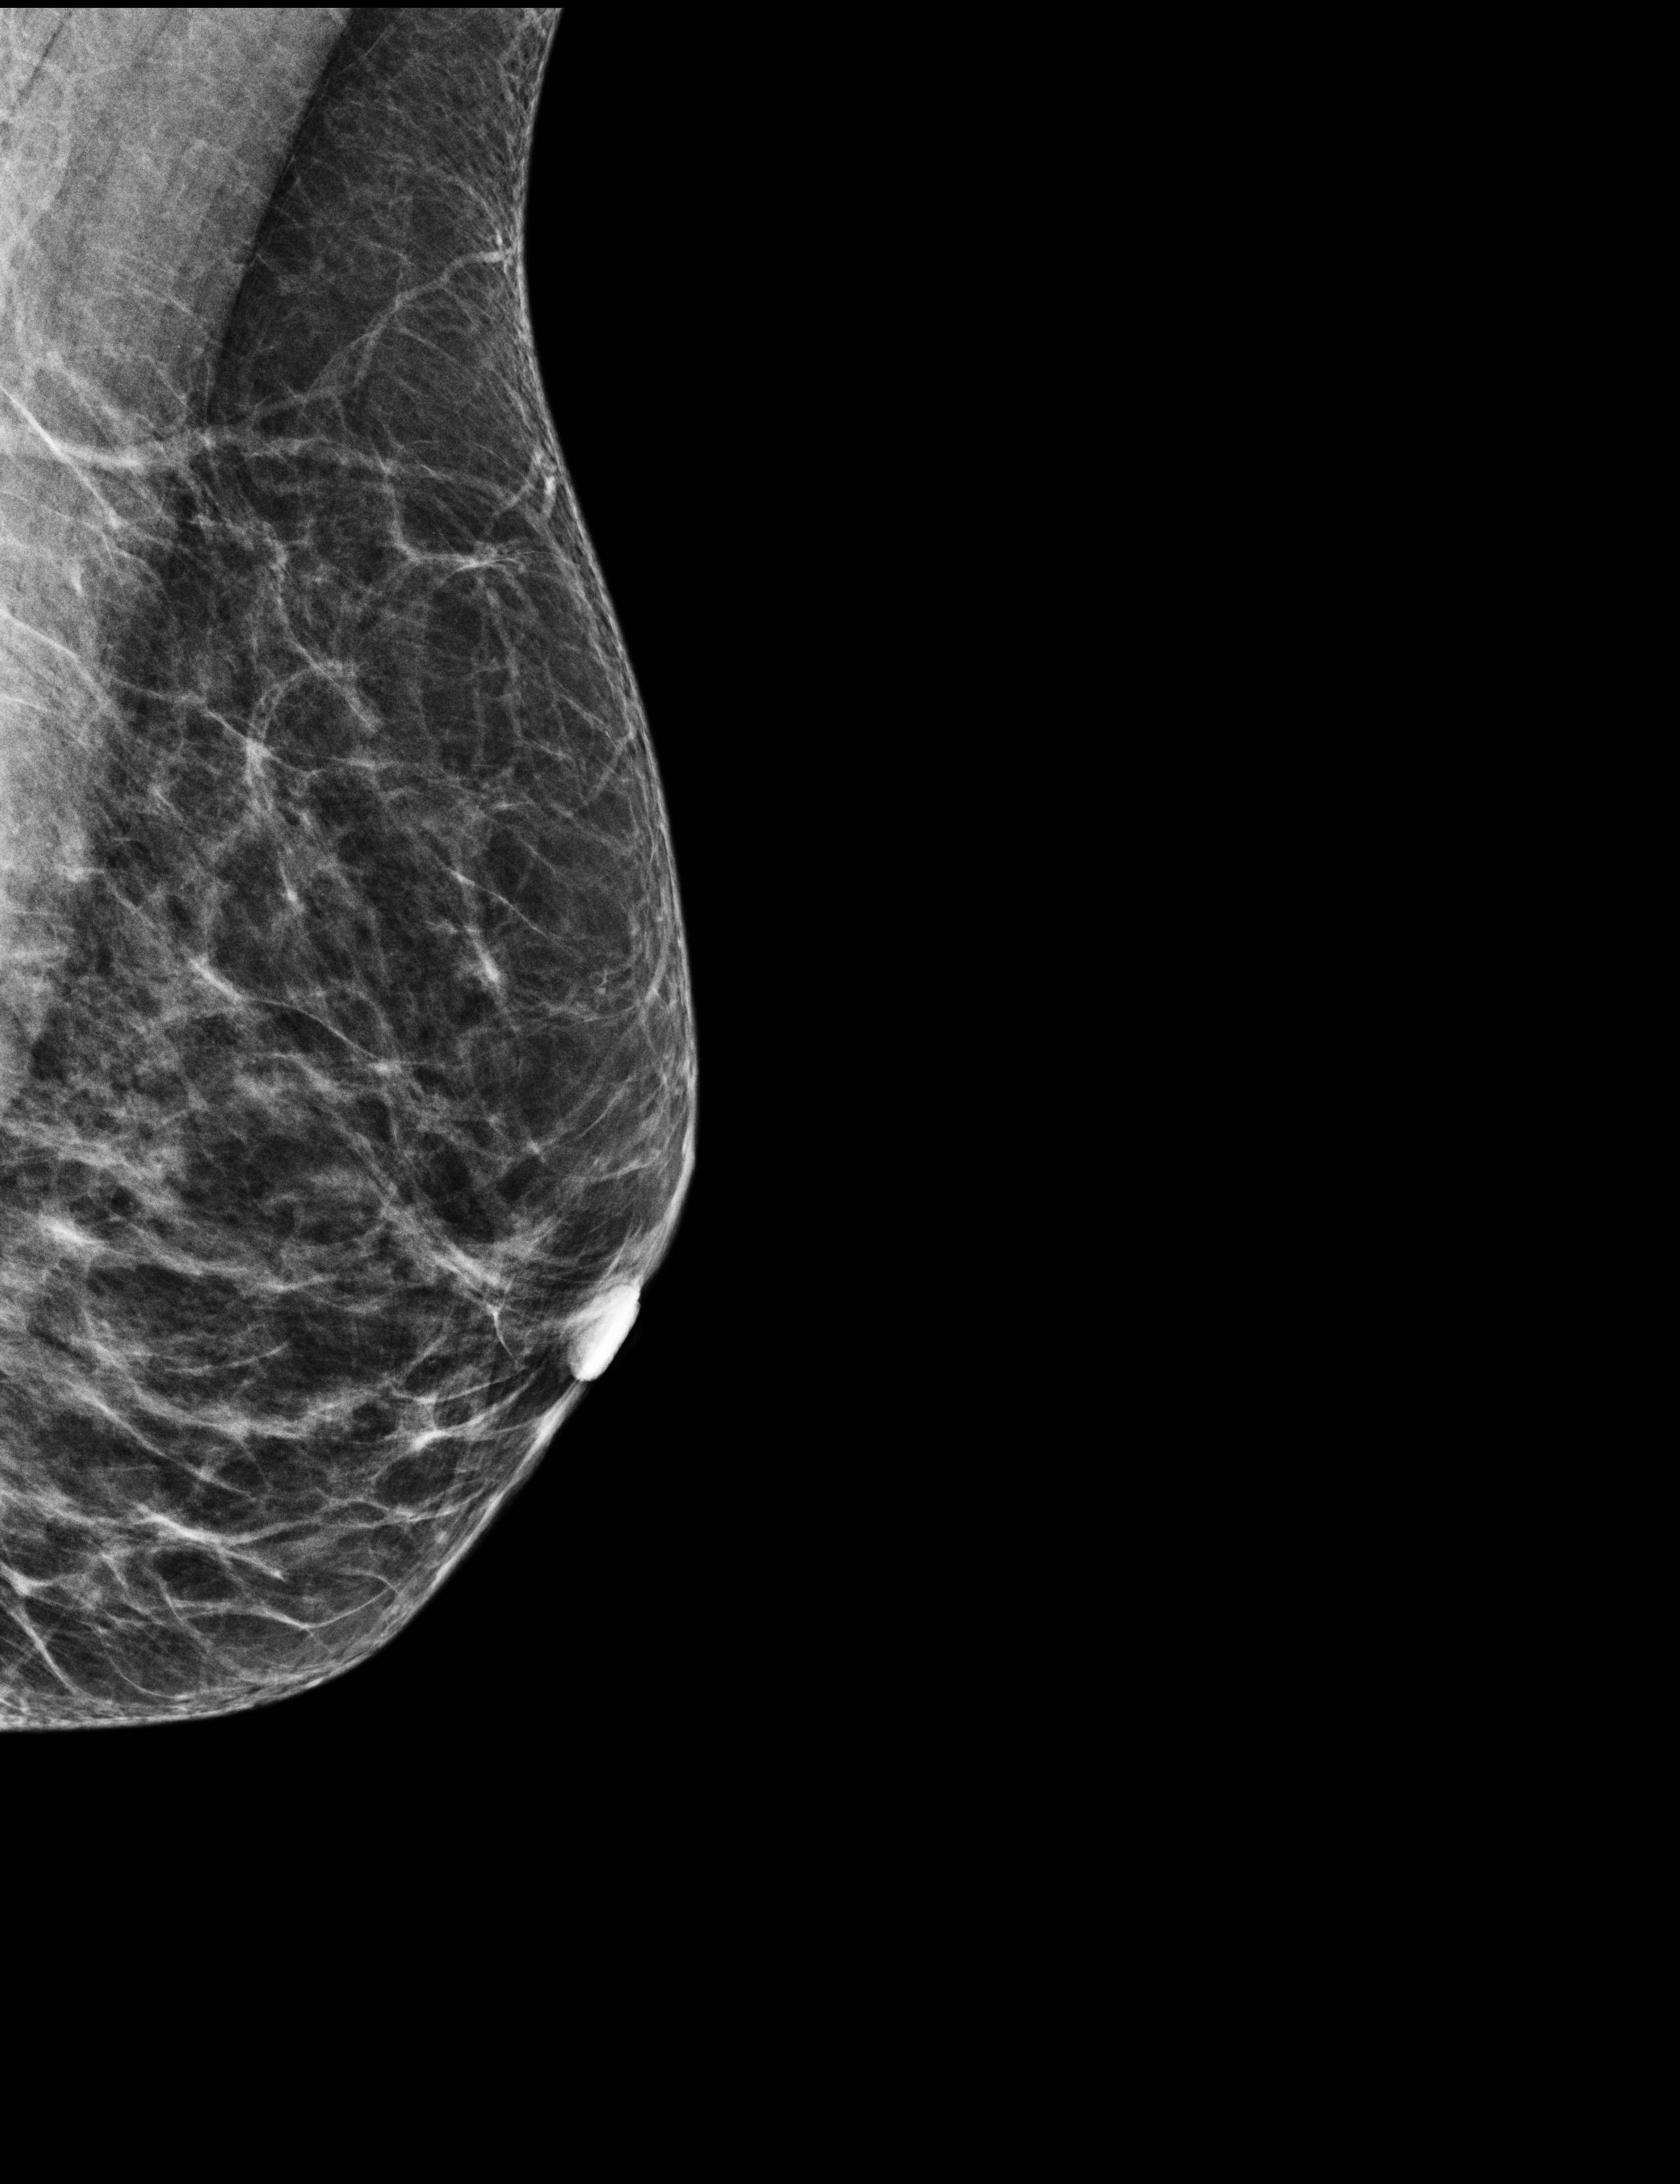
Screening examination. Patient: female, 65 years.
Image type: full-field digital mammogram. Breast: left. Projection: medio-lateral oblique projection.